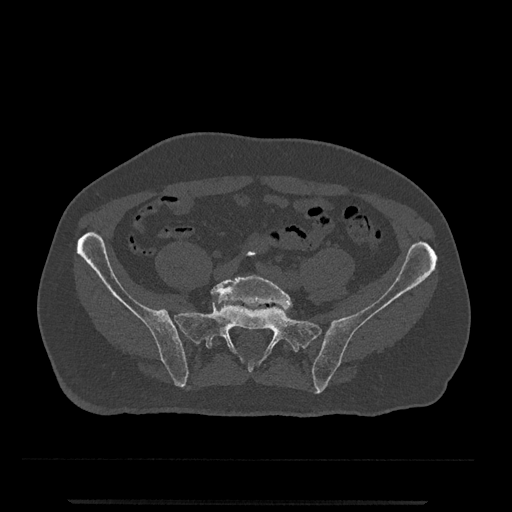
CT including the spine, one axial slice. Position 32 of 797 along the scan axis. Bone window (W 1800 / L 400 HU). 0.5 mm slice thickness. 512 × 512 image matrix, field of view 419 × 419 mm. Patient: male, 63 years. From the clinical record (not read from this slice): primary cancer: prostate.
Outlined on this slice (semi-automatic segmentation, software-assisted and operator-edited):
- L5 vertebra: box from (x=211, y=274) to (x=293, y=350) px